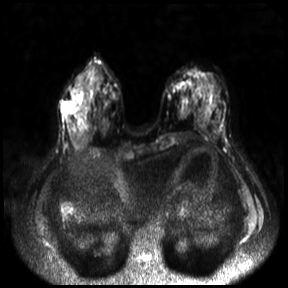
Breast MRI, one axial slice; slice 11 of 30 in the series (ordered by position); diffusion-weighted series; image 2 of 4 stored at this slice position (different b-values; order by instance number); 3 T; 288 × 288 image matrix. Female patient.
Annotated regions visible in this slice (expert manual segmentation):
- tumour on diffusion-weighted imaging: box from (x=62, y=100) to (x=78, y=114) px